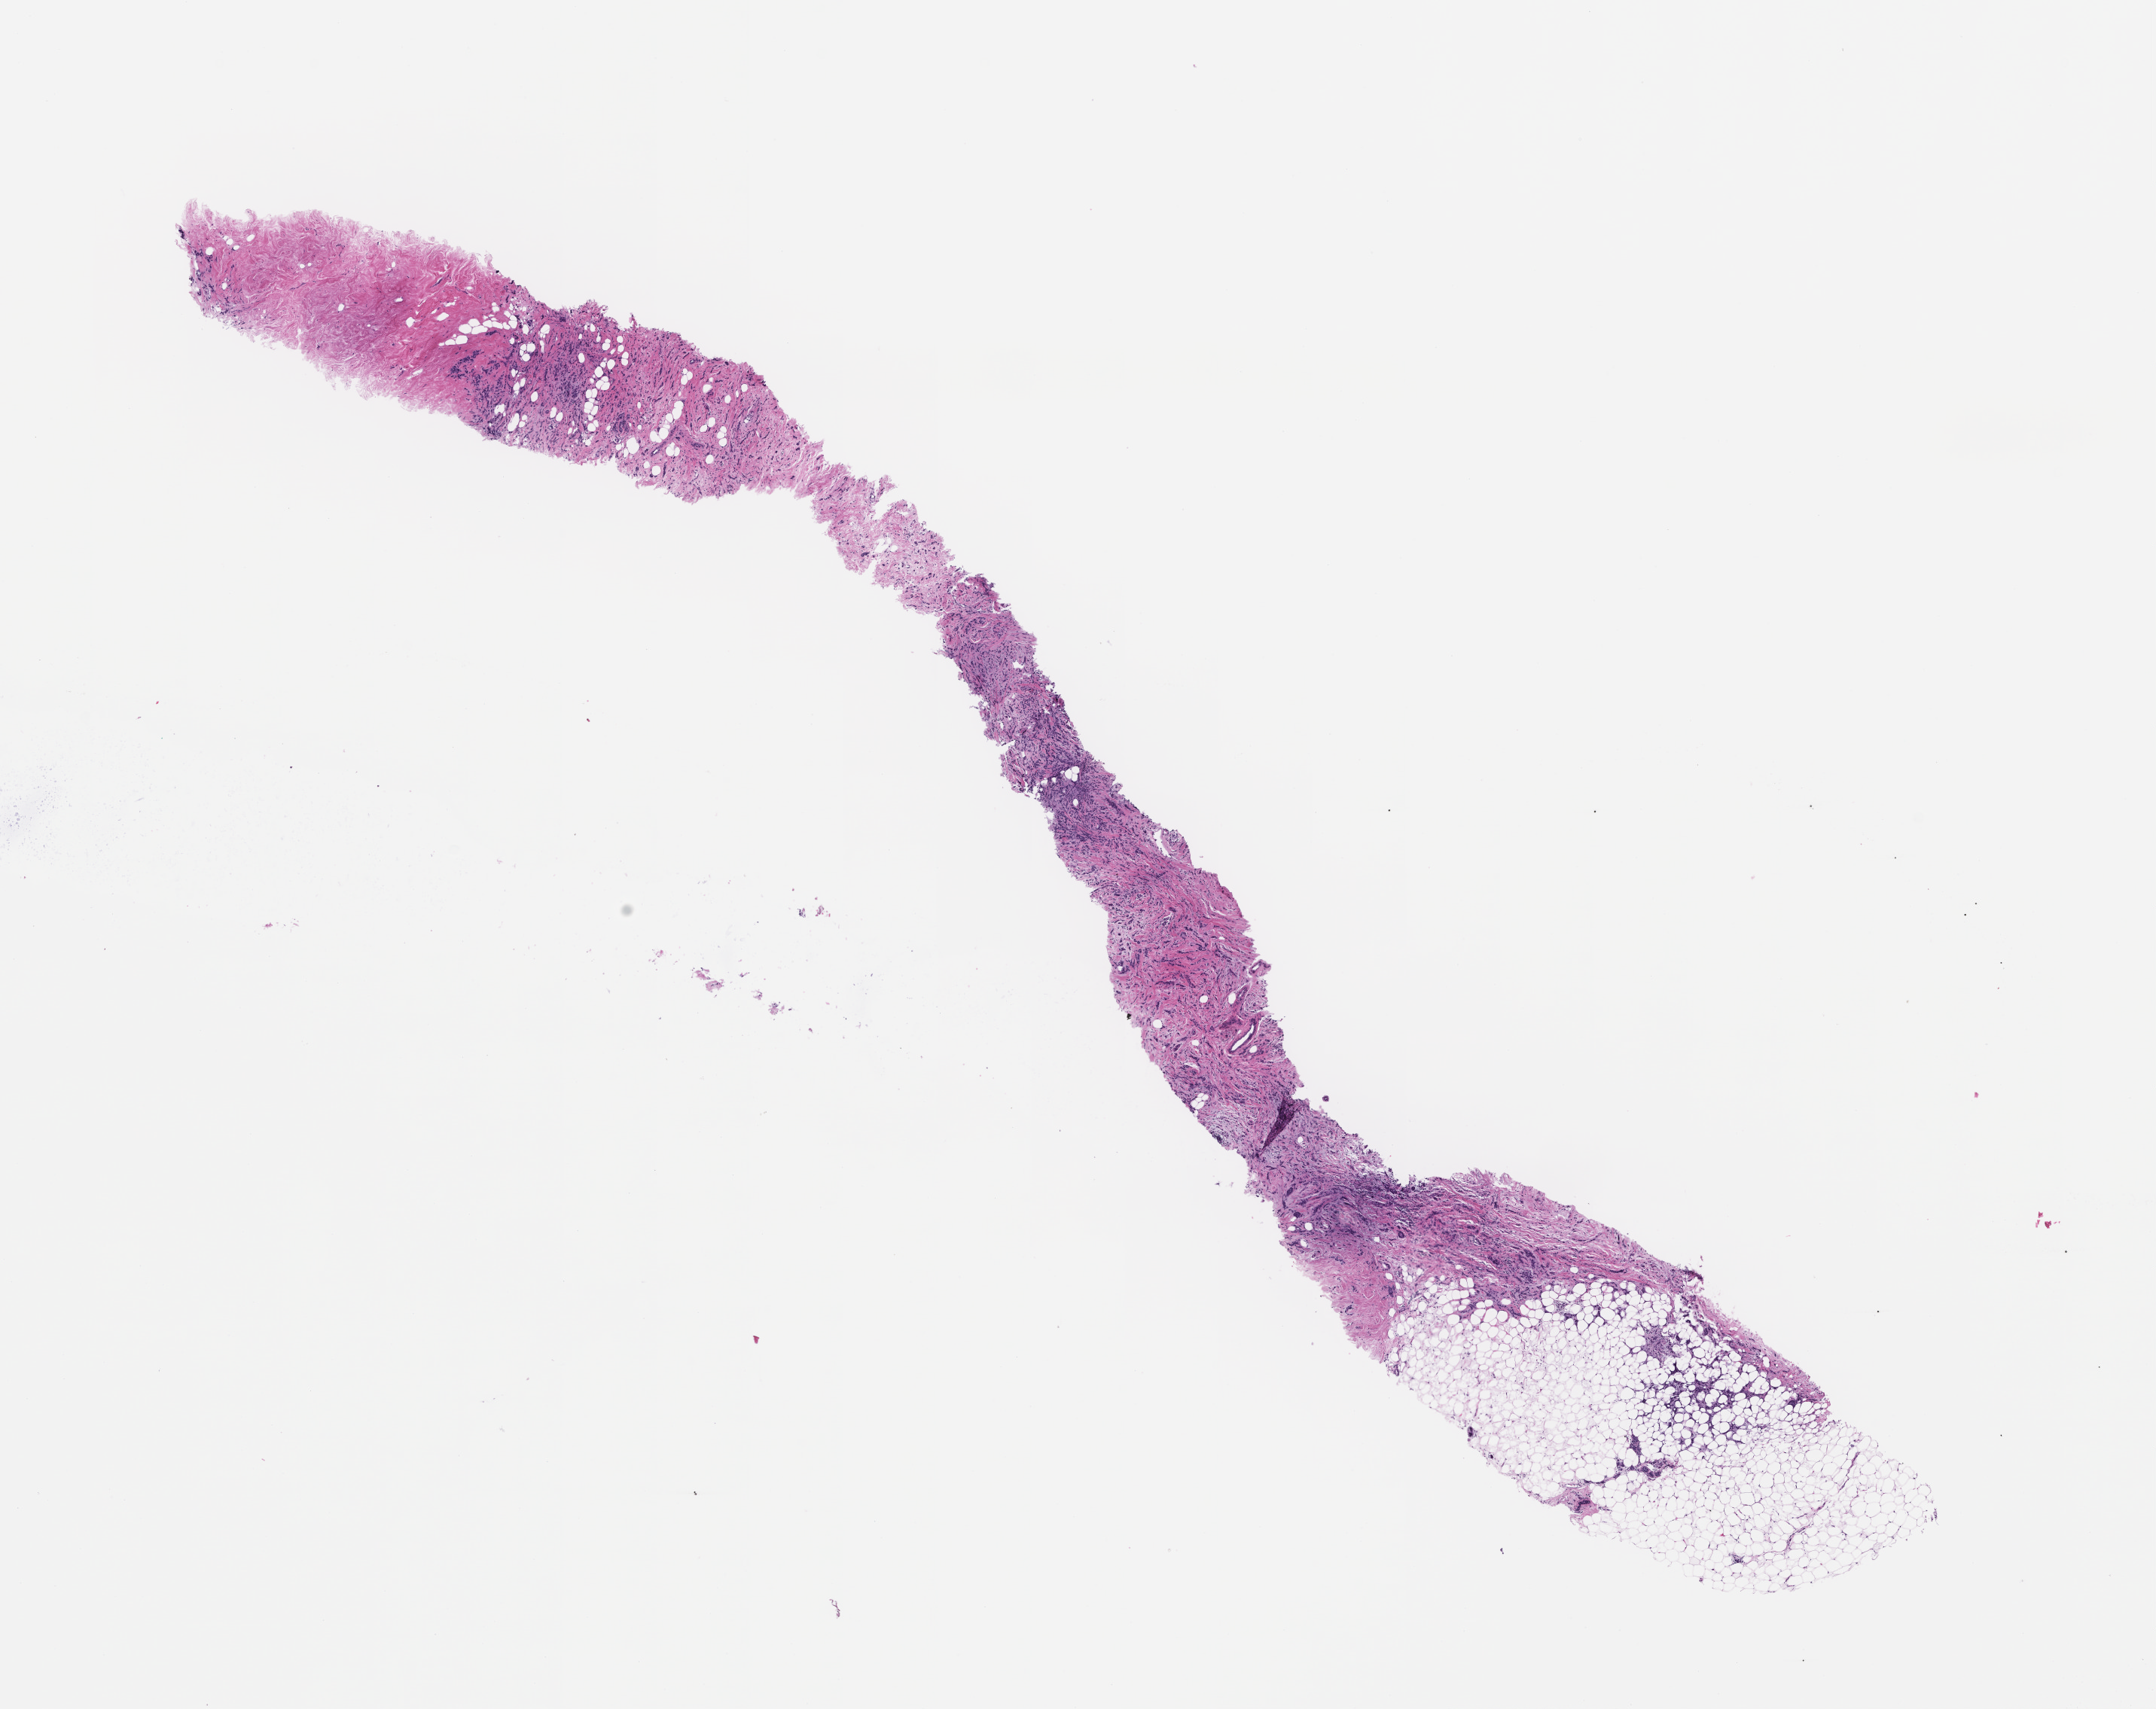
Whole-slide image, haematoxylin and eosin stain — low-resolution overview of the scanned area, about 11.6 x 9.2 mm; formalin-fixed paraffin-embedded section; site: breast. Female patient.
- this section: primary tumor
- diagnosis: Invasive Breast Carcinoma